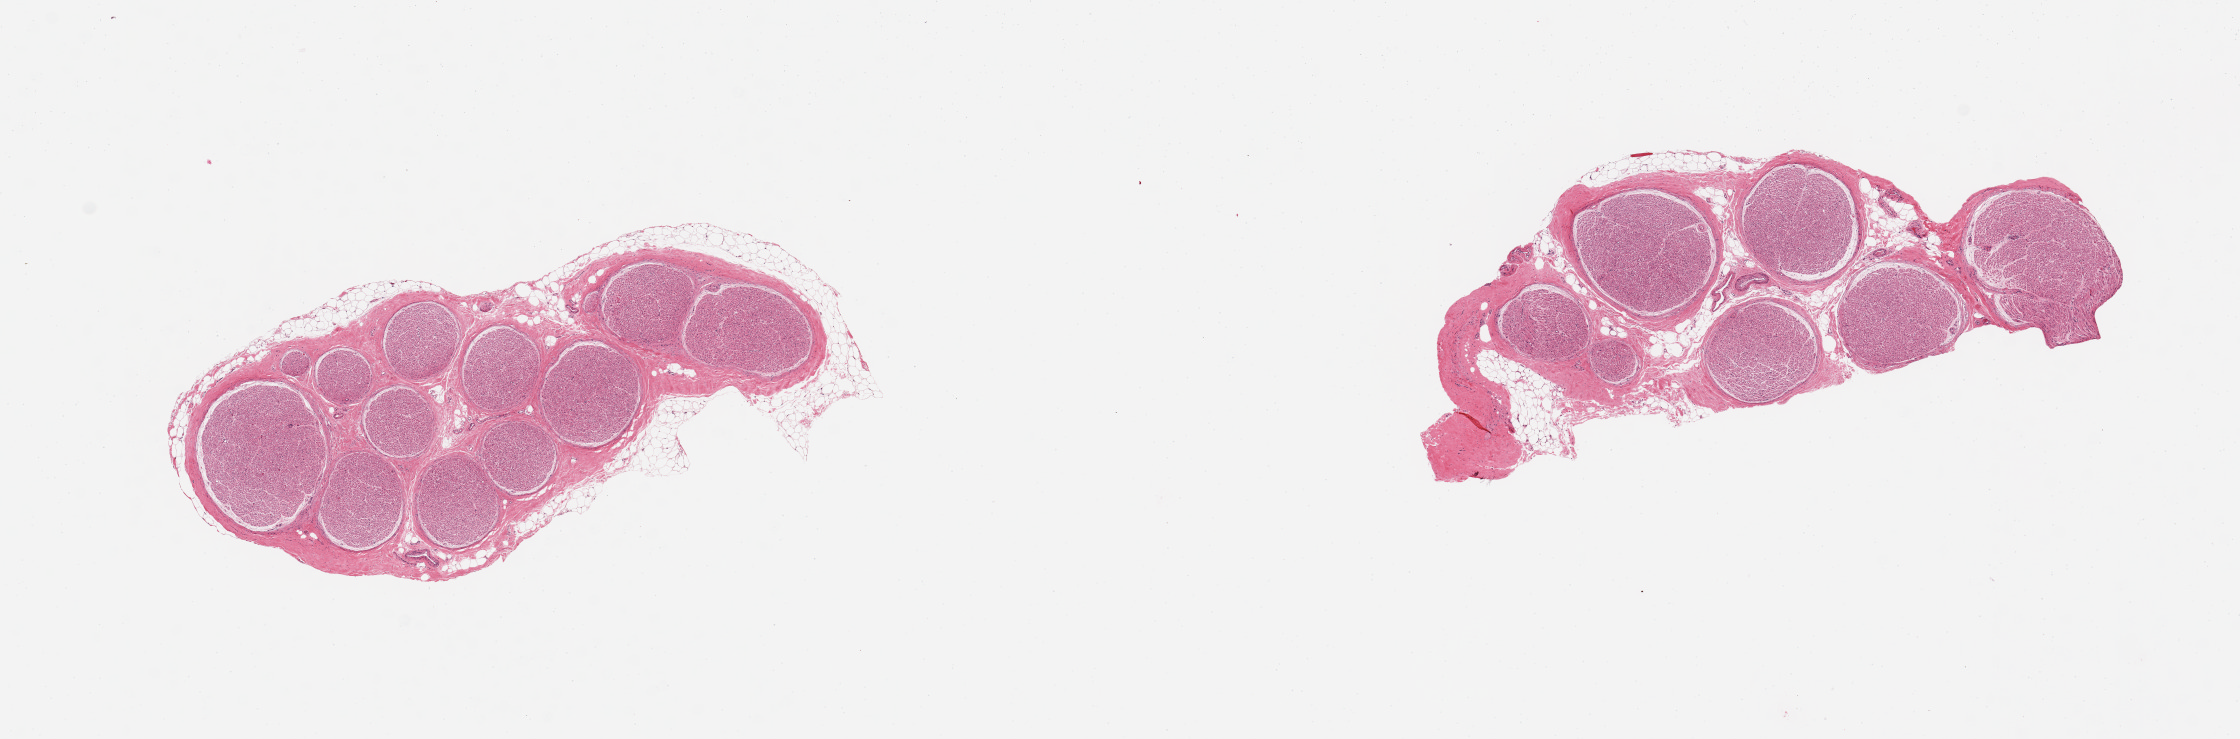
Digitized H&E-stained section, brightfield — a low-resolution overview of the entire scanned area, about 17.7 x 5.8 mm; PAXgene-fixed paraffin-embedded (PFPE) section; target tissue: tibial nerve; donor tissue sample. Donor: female.
Review note (as recorded): 2 pieces; 10% external & internal fat.